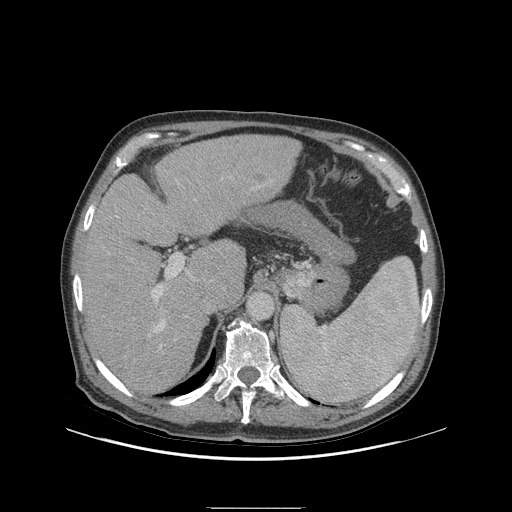
Contrast-enhanced abdominal CT (liver protocol), one axial slice. Slice 63 of 105 in the series (ordered by position). Reconstruction kernel STANDARD. 140 kVp. Soft-tissue window (W 400 / L 40 HU). 512 × 512 image matrix, field of view 440 × 440 mm. Case-level facts recorded for this patient, not image findings: diagnosis: hepatocellular carcinoma (patient treated with transarterial chemoembolisation; whether this scan precedes or follows treatment is not stated here); TNM stage (as recorded): Stage-I; Child-Pugh class: A; tumour nodularity: uninodular; tumour size: 5.1 cm.
Structures marked on this image (semi-automatic segmentation, software-assisted and operator-edited):
- liver parenchyma outside the tumour (the mass and vessels are separate outlines, so this box may not span the whole liver): bounding box <80,134,300,394> (left, top, right, bottom; pixels)
- mass: <252,159,274,182>
- liver vessels: <151,181,261,349>